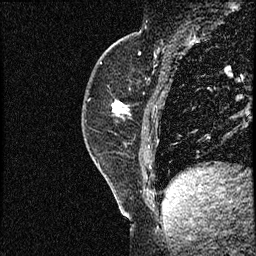
Breast MRI (dynamic contrast-enhanced), one sagittal slice; slice 22 of 56 in the series (ordered by position); dynamic contrast-enhanced study with each time point stored as its own series, time point 2 of 3 at this slice position (early post-contrast, ordered by acquisition time); 1.5 T; TE 4.2 ms, TR 17.3 ms; 2 mm slice thickness; 256 × 256 image matrix, field of view 200 × 200 mm. Female patient. Case-level facts recorded for this patient, not image findings: setting: breast cancer imaged before/during neoadjuvant chemotherapy; receptor status: HER2-positive.
Annotated regions visible in this slice (semi-automatically segmented with operator editing):
- analysis volume of interest (the breast-tissue region the enhancement analysis was run in; not a lesion): bounding box <82,50,156,155> (left, top, right, bottom; pixels)
- tumour enhancement mask (voxels above the 100 % enhancement threshold inside the analysis volume of interest): <113,102,127,114>